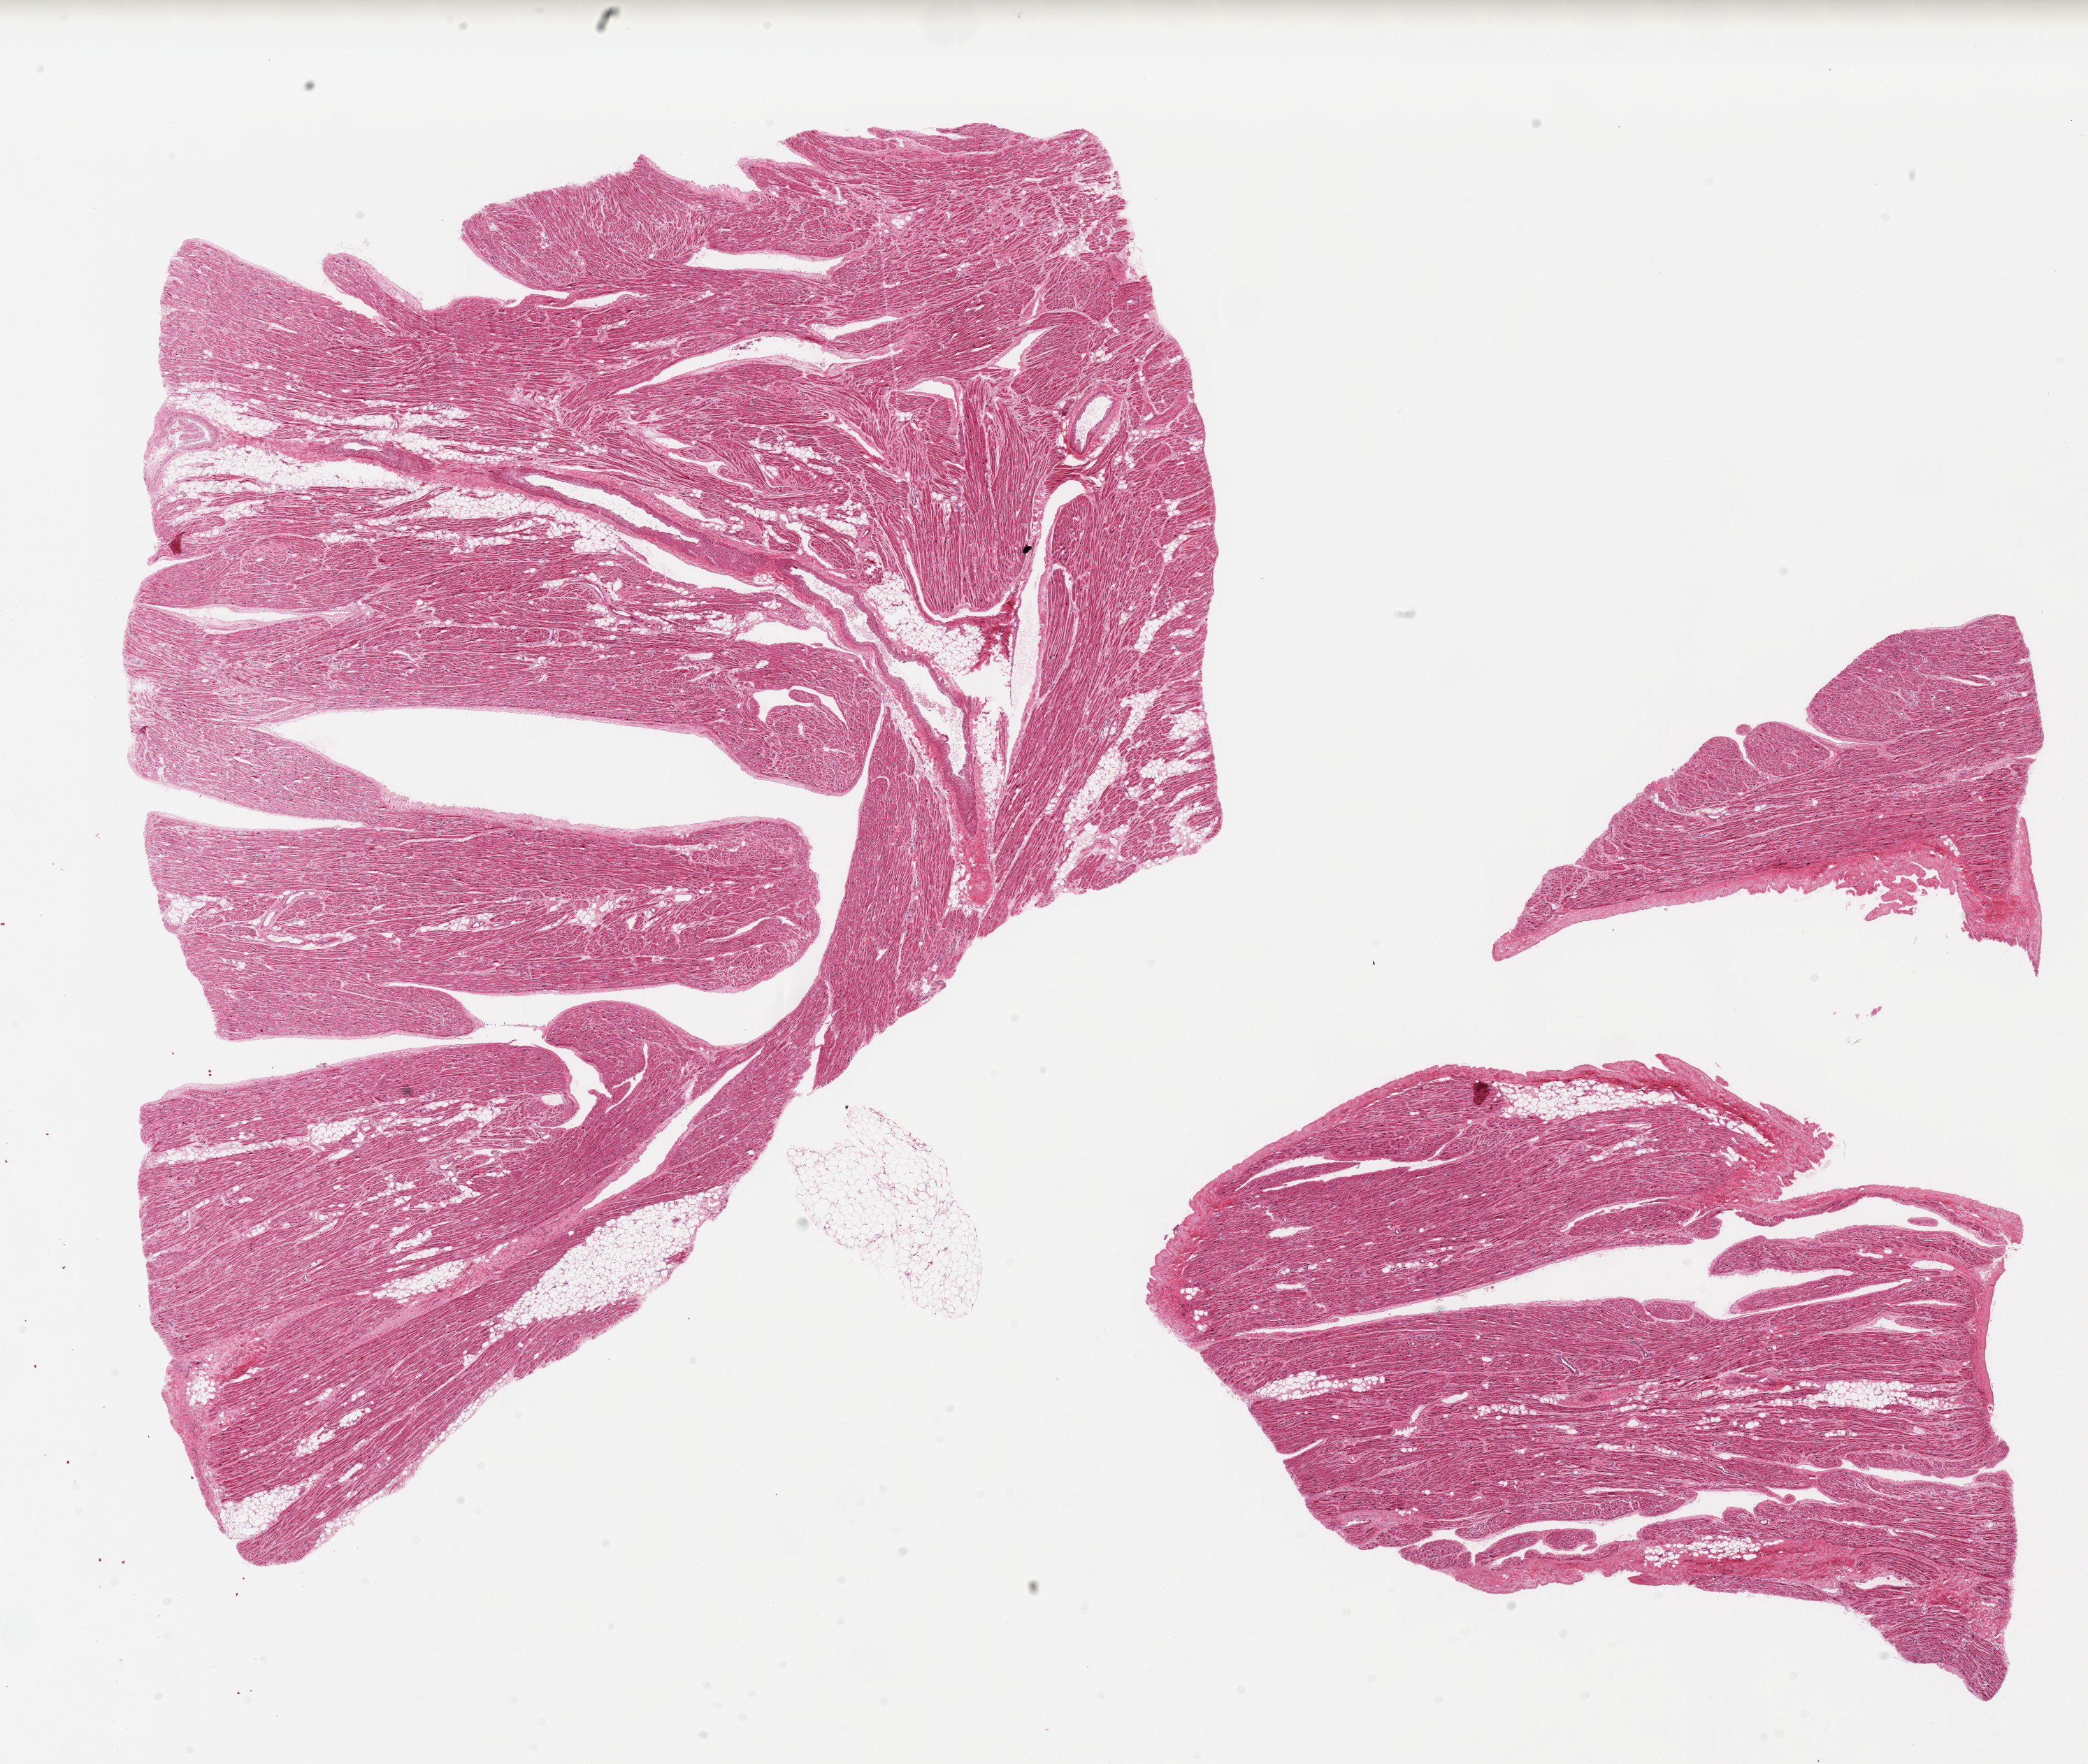
H&E whole-slide image, brightfield — whole scanned area (about 23.6 x 20.0 mm, from a 20x scan) shown as a low-resolution overview, PAXgene-fixed, paraffin-embedded tissue, section of auricular appendage (target tissue), tissue donor sample. Donor sex: male.
Review note (as recorded): 2 pieces, no abnormalities.